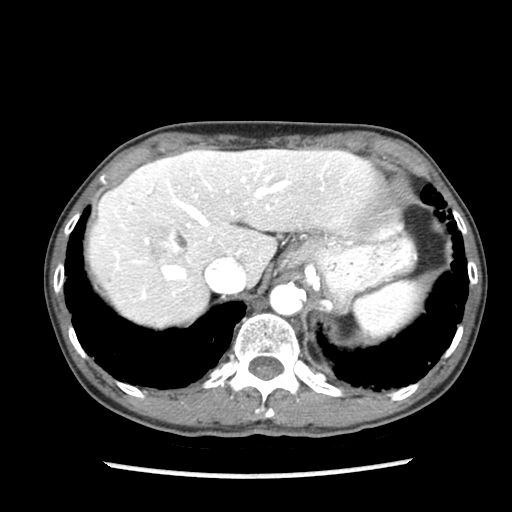
Contrast-enhanced abdominal CT (liver protocol), one axial slice. Slice 65 of 87 in the series (ordered by position). Reconstruction kernel STANDARD. Soft-tissue window (W 400 / L 40 HU). 512 × 512 image matrix, field of view 300 × 300 mm. Case-level facts recorded for this patient, not image findings: diagnosis: hepatocellular carcinoma (patient treated with transarterial chemoembolisation; whether this scan precedes or follows treatment is not stated here); TNM stage (as recorded): Stage-IIIB; Child-Pugh class: A; tumour differentiation: well differentiated; tumour nodularity: uninodular.
Outlined on this slice (semi-automatic segmentation, software-assisted and operator-edited):
- liver parenchyma outside the tumour (the mass and vessels are separate outlines, so this box may not span the whole liver): bounding box [x1, y1, x2, y2] px = [88, 149, 378, 326]
- mass: [148, 227, 187, 262]
- liver vessels: [102, 159, 323, 298]